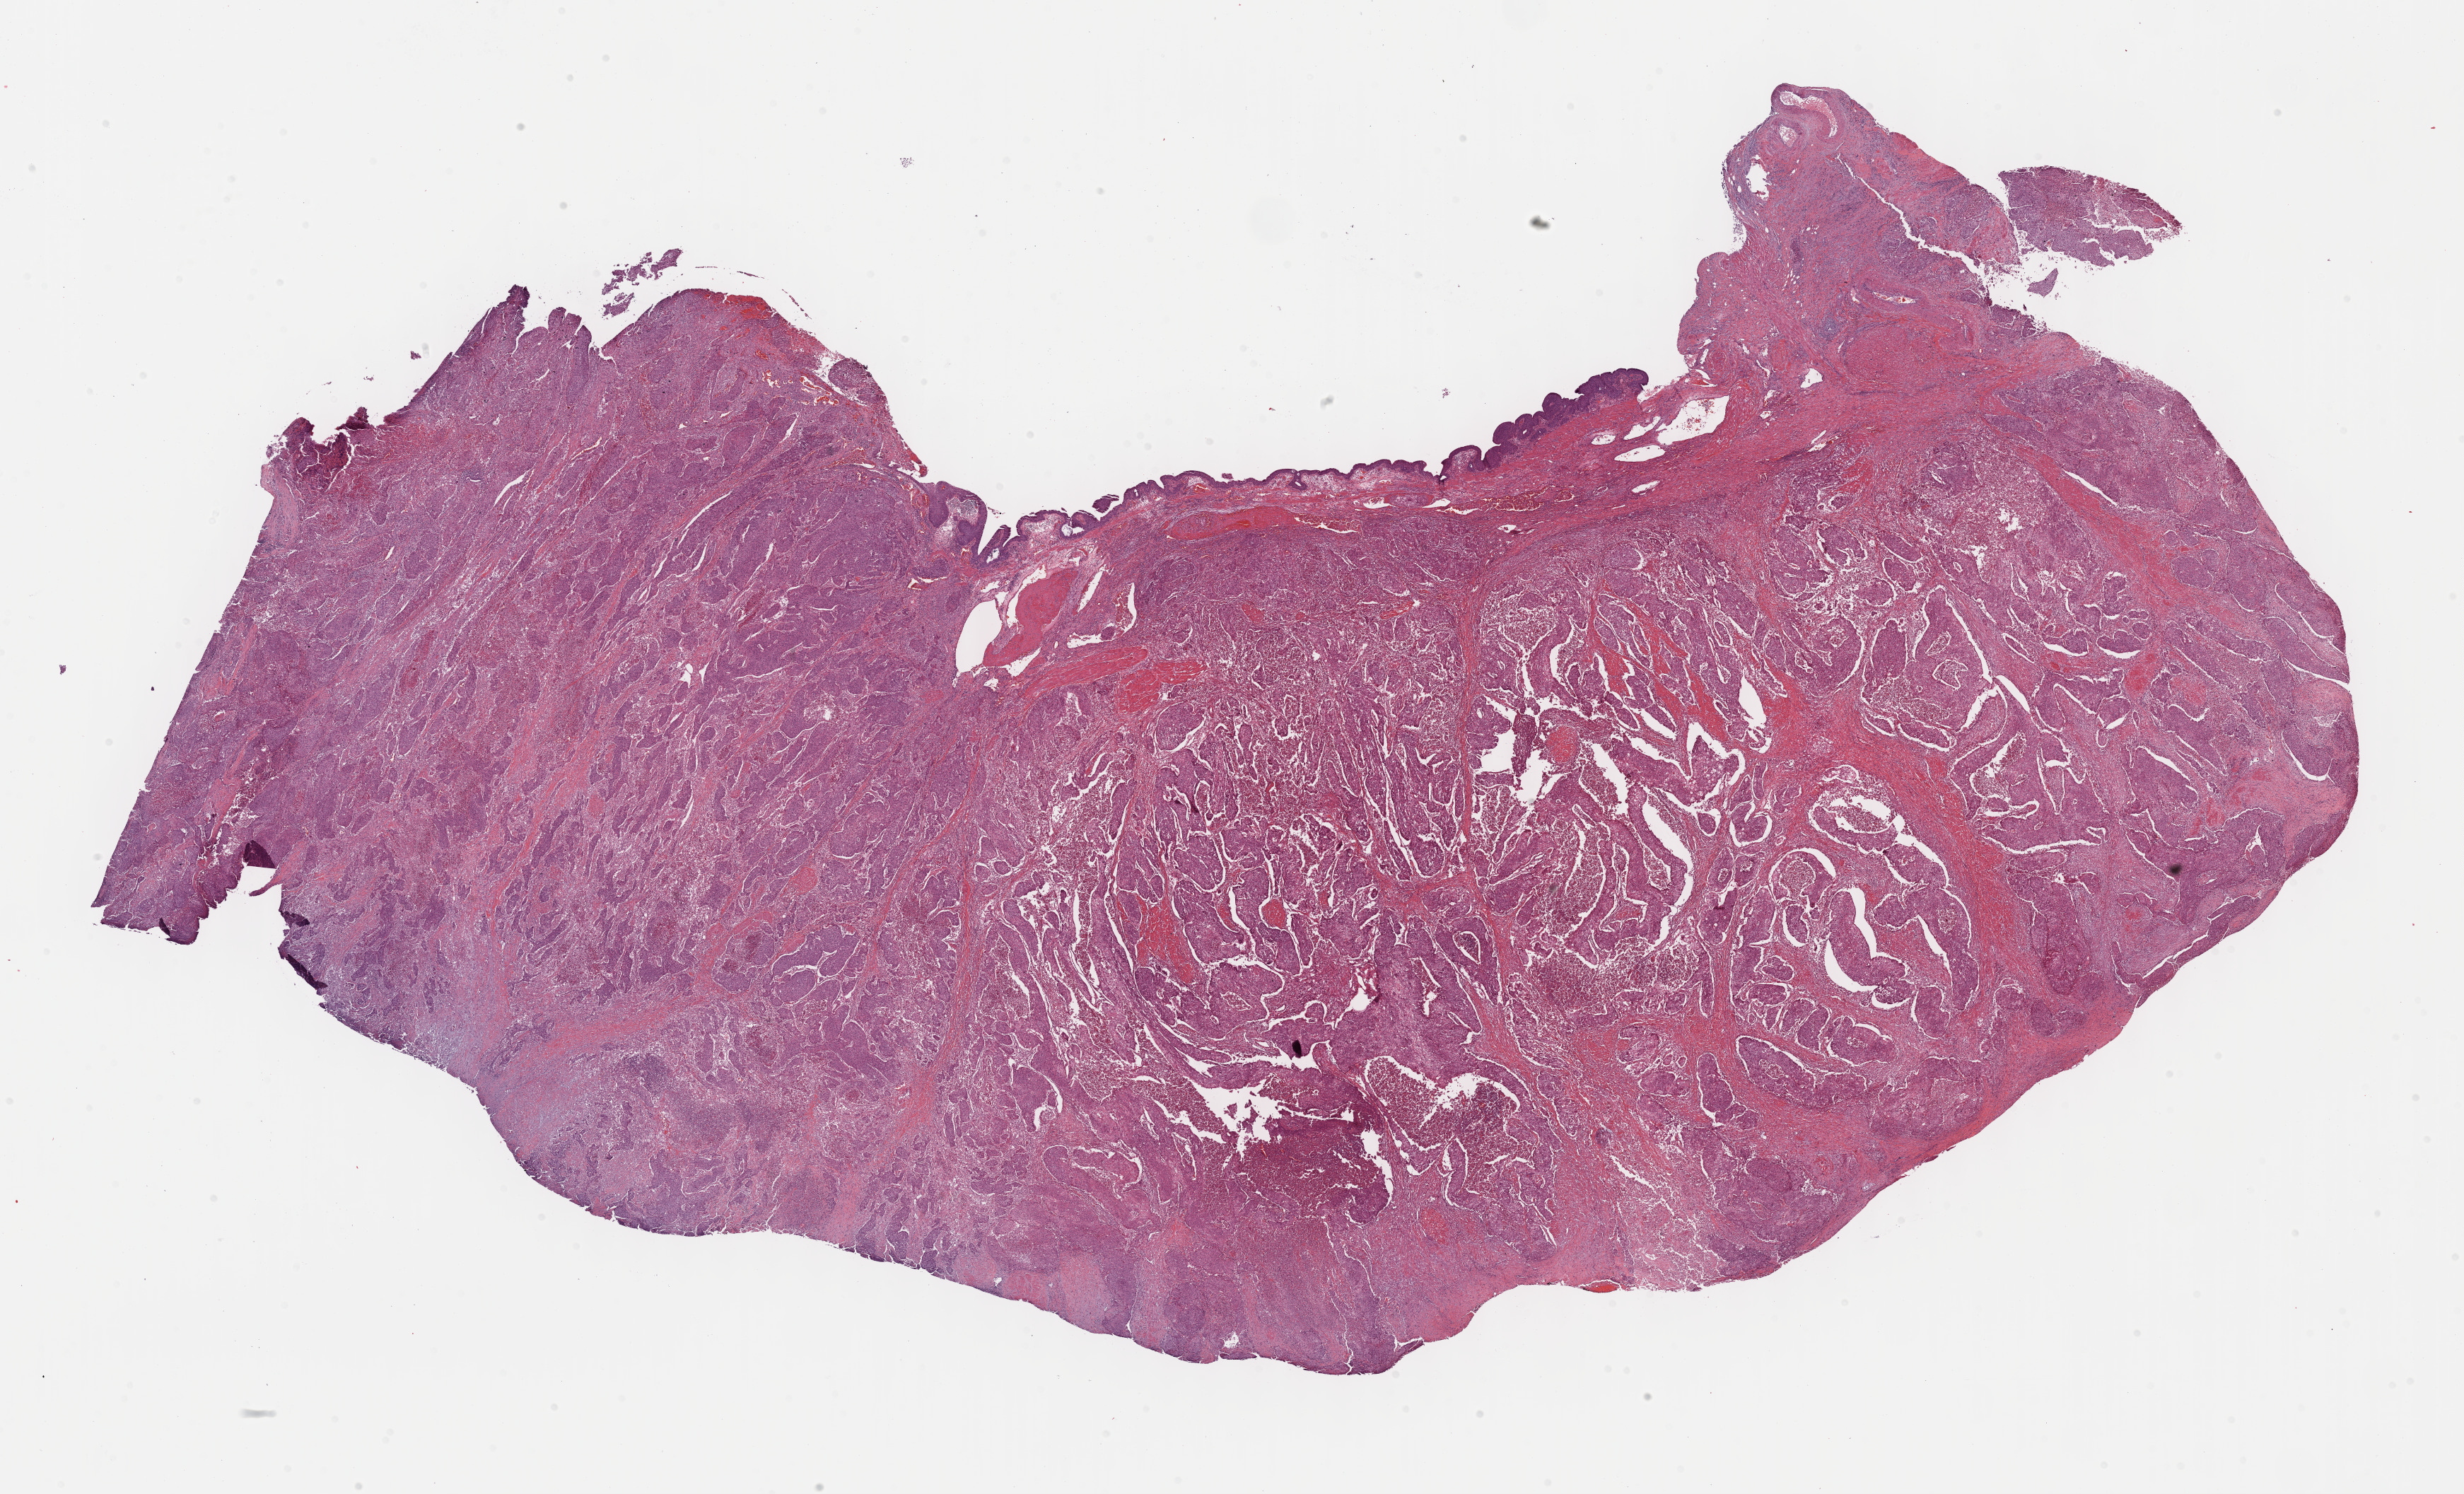
Whole-slide histology image, H&E-stained, shown as a low-resolution overview of the whole scanned area (about 28.2 x 17.1 mm, from a 40x scan). Formalin-fixed paraffin-embedded (FFPE) diagnostic section. Primary tumour sample from the bladder. Patient: male, age at initial diagnosis 64 years. Histologic grade: high grade.
- AJCC pathologic stage: III (4th edition)
- lymph nodes positive (case pathology): 0 of 17 examined
- pathologic diagnosis: Transitional cell carcinoma